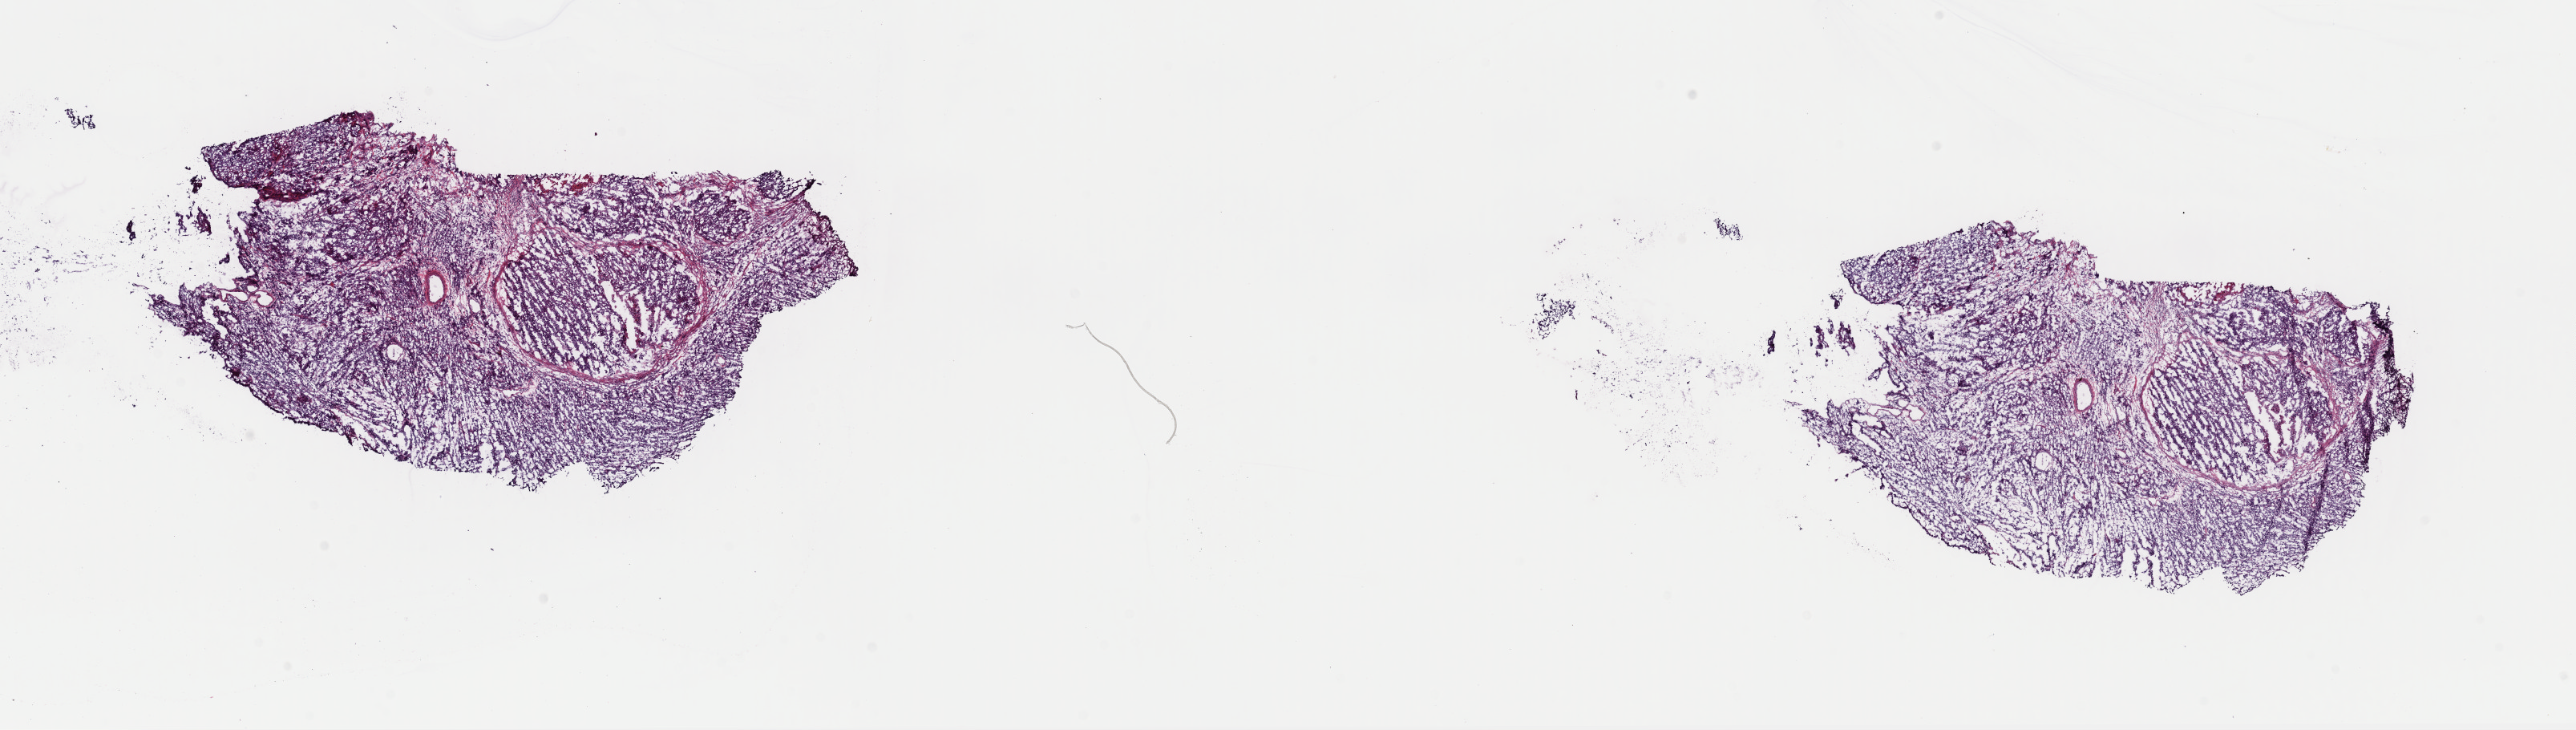
Digitized H&E-stained tissue section (whole slide) — low-resolution overview of the scanned area, about 25.4 x 7.2 mm (acquisition: 40x scan); frozen section from the top of the tissue portion; sample: primary tumour, bladder. Male patient; age at initial diagnosis 64 years. Histologic grade: high grade. Slide review estimates, as recorded: tumour cells 85%, tumour nuclei 80%, normal cells 0%, stromal cells 15%, necrosis 0%. Infiltration values recorded for this section: lymphocyte infiltration 0%, monocyte infiltration 0%, neutrophil infiltration 0%.
* pathologic diagnosis: Transitional cell carcinoma
* AJCC pathologic stage: IV (7th edition)
* lymph nodes positive (case pathology): 5 of 18 examined